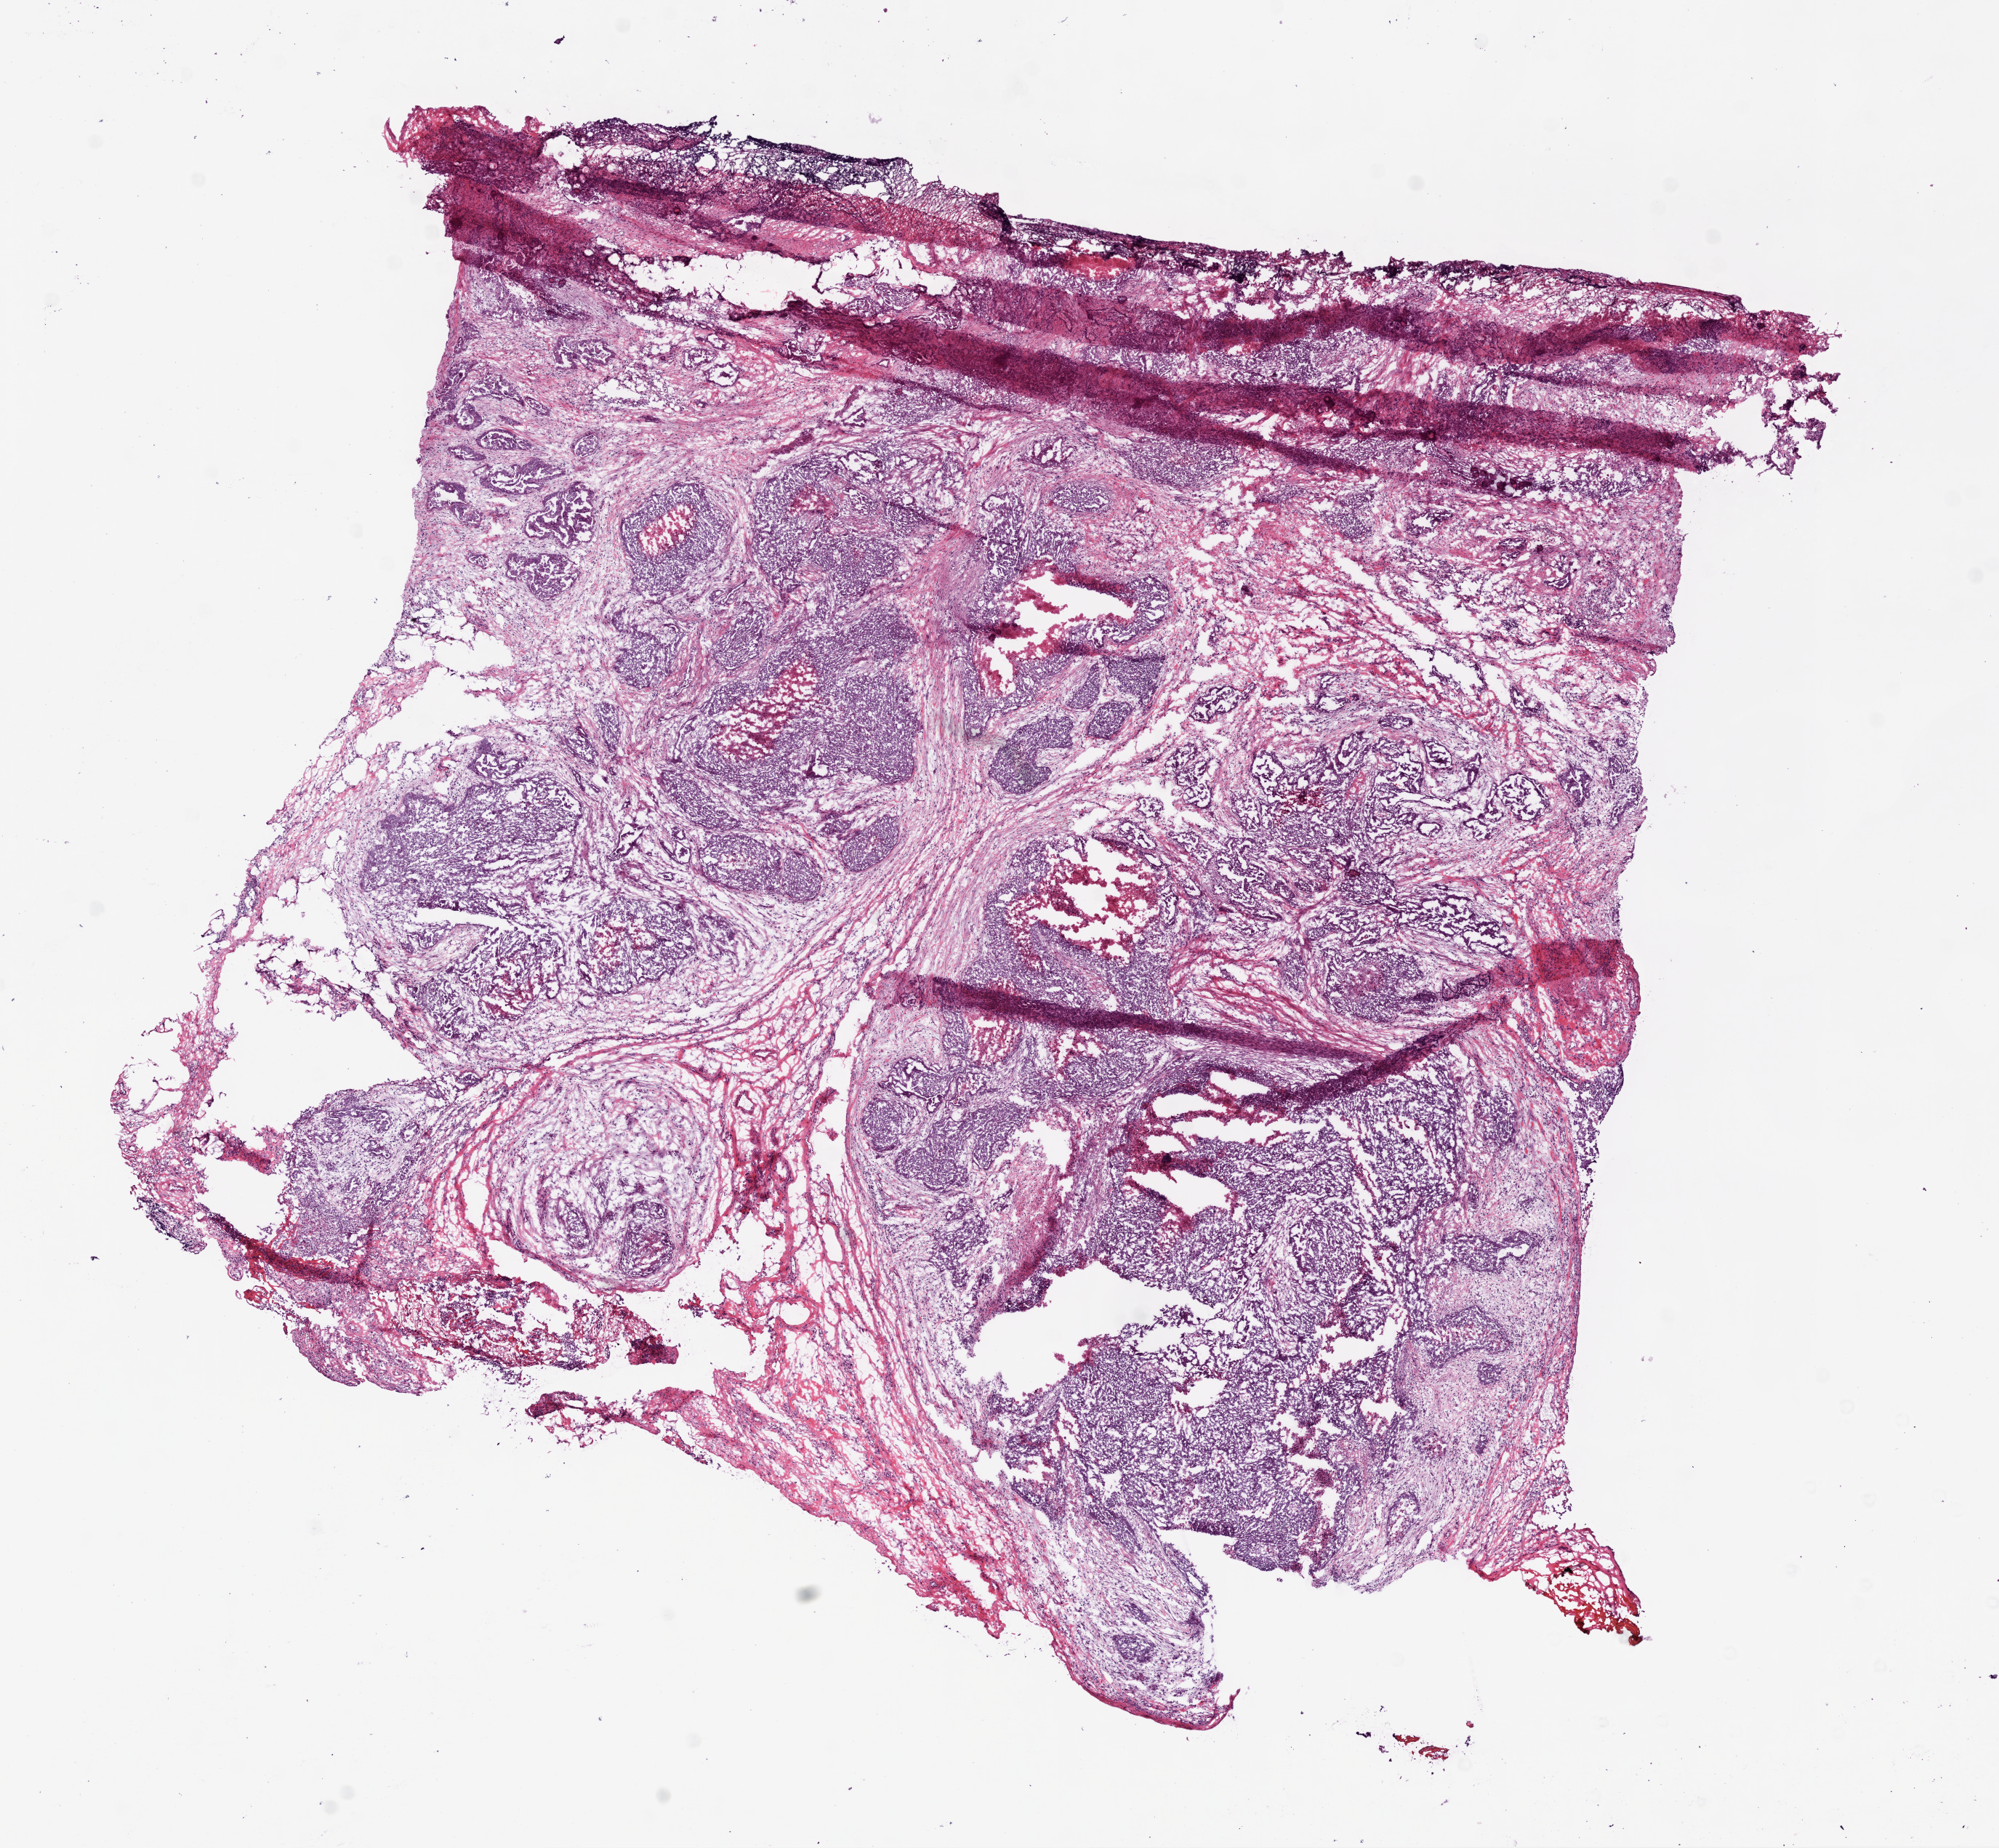
Whole-slide histology image, H&E — a low-resolution overview of the entire scanned area, about 11.0 x 10.2 mm (from a 20x scan). Frozen section. Sample: primary tumour, ovary. Patient: female, age at initial diagnosis 73 years. Histologic grade: G3 (poorly differentiated). Pathologist review of this section (percent, as recorded): tumour cells 40%, tumour nuclei 70%, normal cells 0%, stromal cells 55%, necrosis 5%.
• pathologic diagnosis: Serous cystadenocarcinoma, NOS
• FIGO stage: IIIC